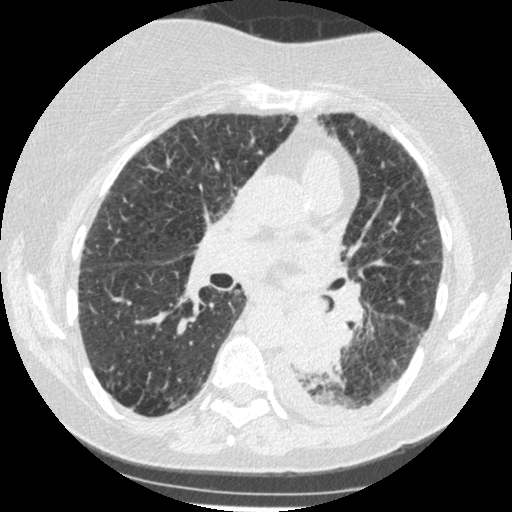
Axial slice from a low-dose chest CT screening exam. Third screening round (two years after baseline). Lung window (W 1500 / L -600 HU). 1.25 mm slice thickness. Female participant, aged 60 years at enrolment. Former smoker at enrolment.
Expert reader's lesion annotation, bounding box <272,306,342,374> (left, top, right, bottom; pixels). Reader record for this screening exam (exam-level; its link to the box is not recorded): non-calcified nodule or mass ≥4 mm, left lower lobe, 54 × 38 mm, smooth margins, soft tissue attenuation, pre-existing on the prior screen: yes; interval growth: yes. Official screen result: positive, other. Later outcome: lung cancer diagnosed 15 days after this screen — small cell carcinoma, NOS, left lower lobe, undifferentiated (G4), stage IV (AJCC 6th edition), 69 mm at pathology.